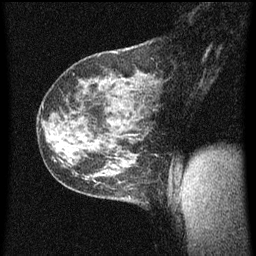
Breast MRI (dynamic contrast-enhanced), one sagittal slice; dynamic contrast-enhanced series, image 2 of 3 at this slice position (ordered by acquisition); 1.5 T; TE 4.2 ms, TR 8 ms; 2 mm slice thickness; 256 × 256 image matrix, field of view 180 × 180 mm. Patient: female, 35 years.
Structures marked on this image (semi-automatic segmentation, software-assisted and operator-edited):
- analysis volume of interest (the breast-tissue region the enhancement analysis was run in; not a lesion): box from (x=106, y=182) to (x=149, y=209) px
- tumour enhancement mask (voxels above the 70 % enhancement threshold inside the analysis volume of interest): (x=128, y=184)–(x=133, y=199)